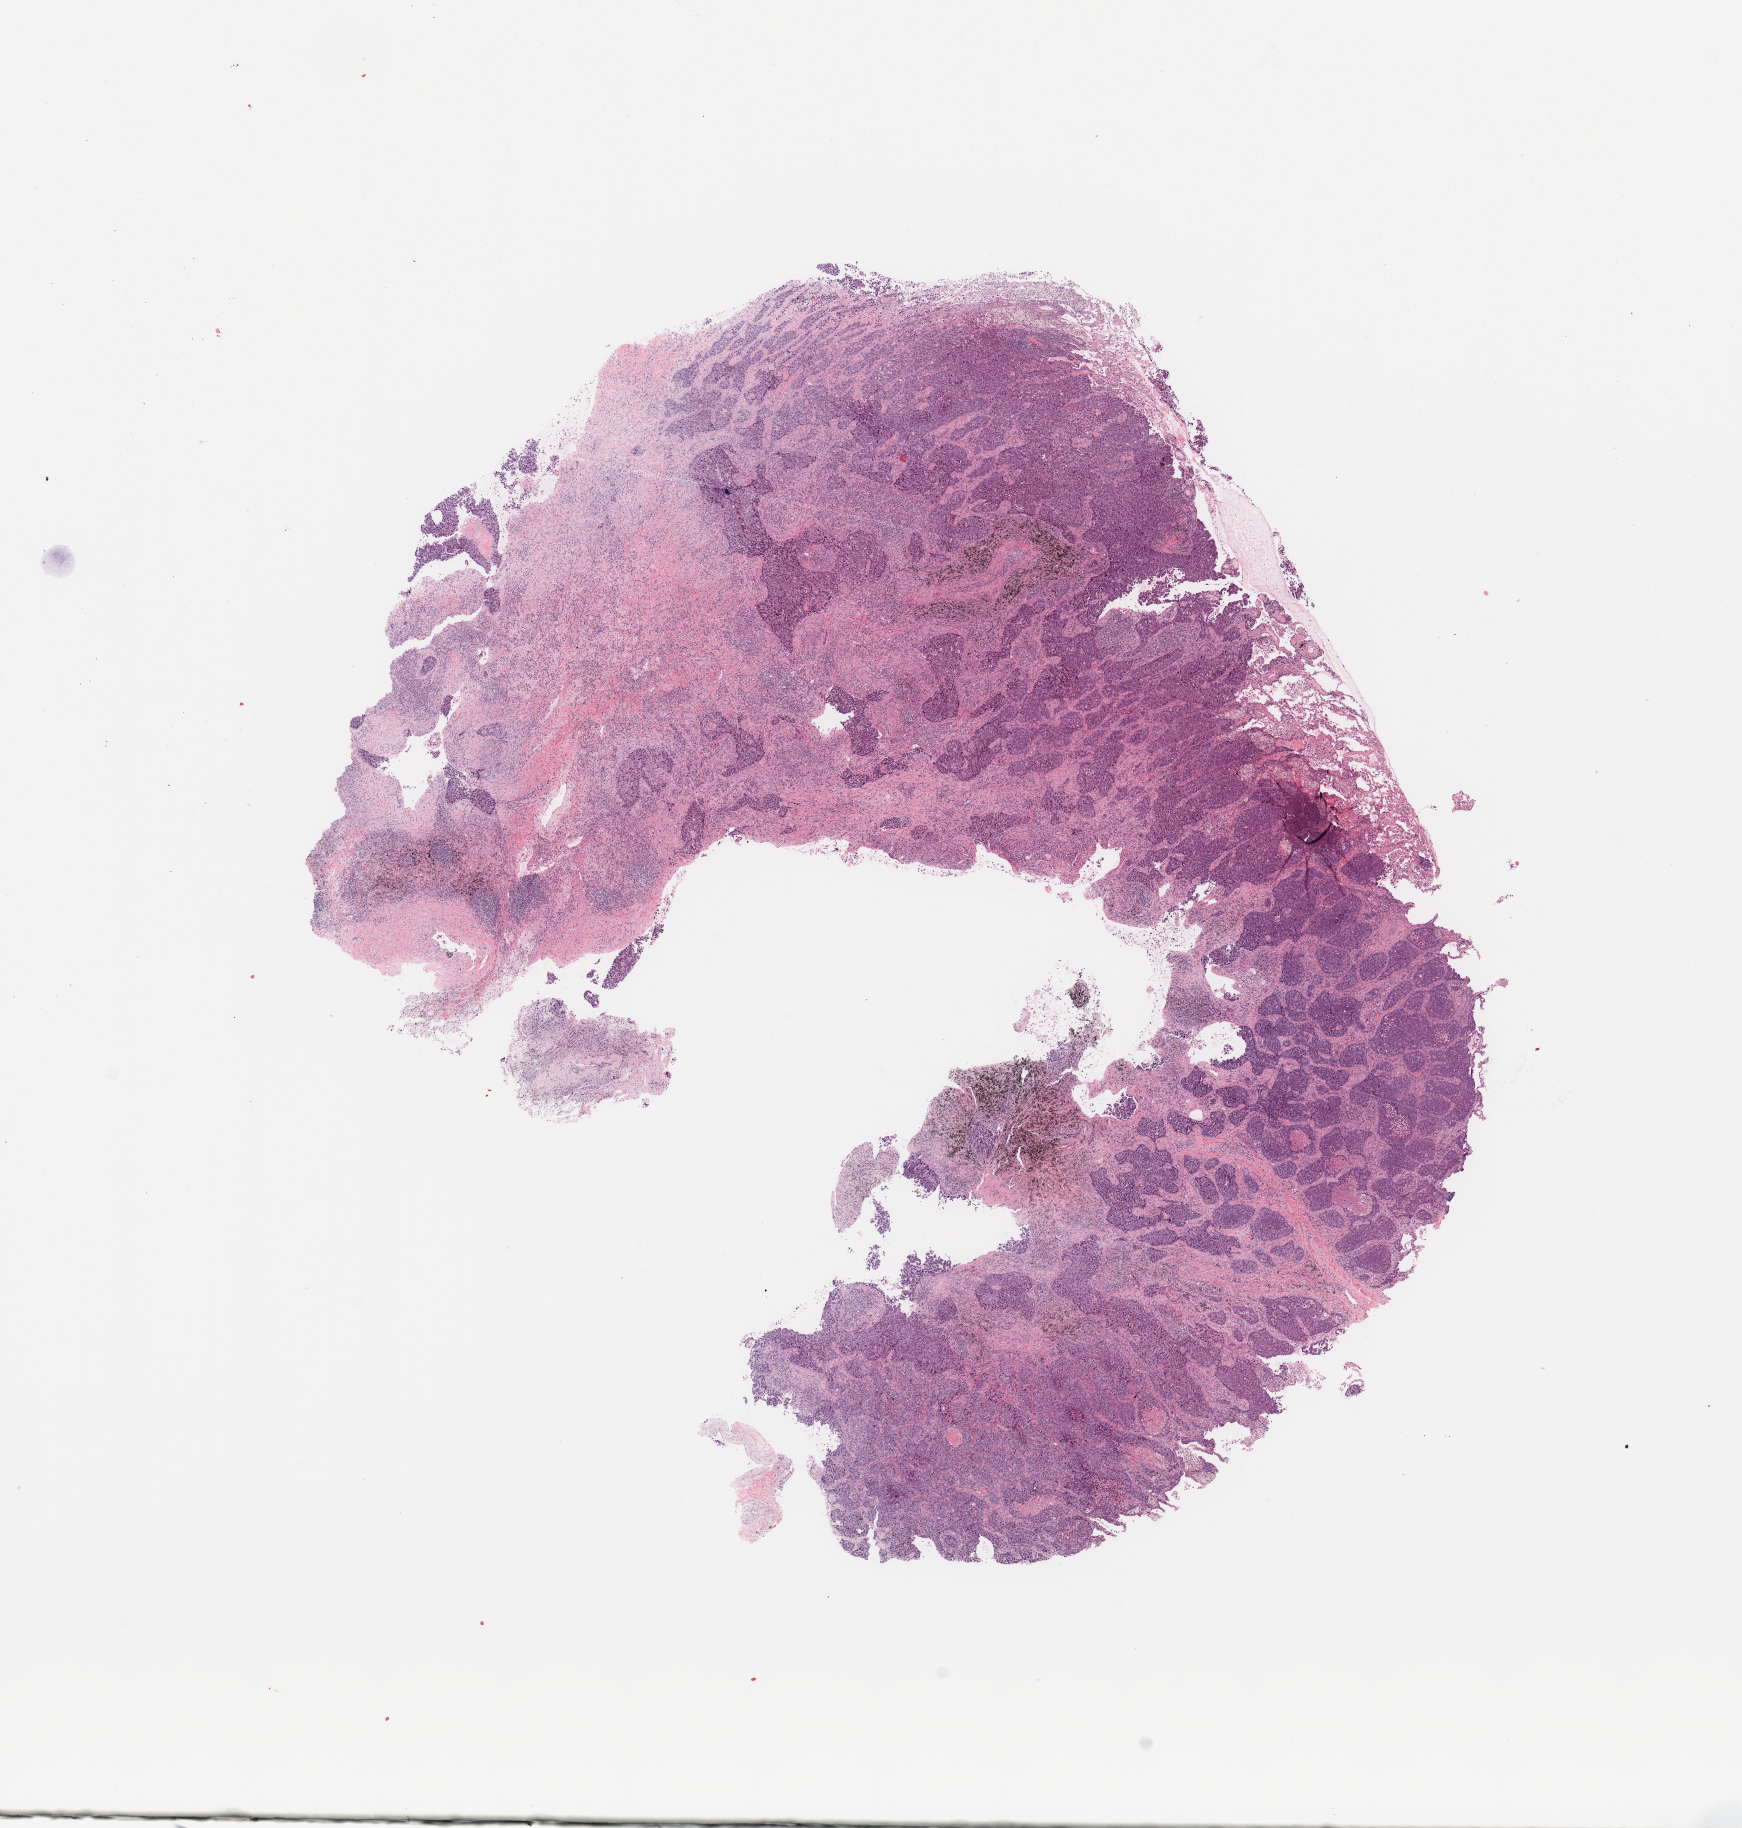
H&E whole-slide image, low-resolution overview of the scanned area, about 13.8 x 14.5 mm. Tumour tissue sample, sampled site: lung. Male, 68 y/o. Histologic grade: G3 (poorly differentiated). Pathologist review of this section (percent, as recorded): tumour nuclei 75%, necrosis 5%.
Histologic diagnosis: Squamous cell carcinoma, NOS. AJCC pathologic stage: IIA. Primary tumour site (as recorded): left upper lobe.